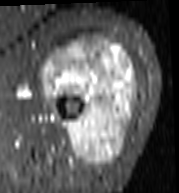
MRI of an extremity soft-tissue mass, one axial slice; position 69 of 103 along the scan axis; STIR; MR volume resampled by the dataset authors to the PET/CT grid (not the native acquisition matrix); 3.27 mm slice thickness; 179 × 193 image matrix, field of view 175 × 188 mm. Female patient. From the clinical record (not read from this slice): histological type: undifferentiated – high grade; grade: high; site of the primary tumour: left thigh.
Annotated regions visible in this slice (expert contour drawn on MRI and transferred to this co-registered scan by the dataset authors):
- gross tumour volume including surrounding oedema: bounding box (x1, y1, x2, y2) in pixels: (43, 35, 140, 168)
- gross tumour volume (mass): (43, 35, 138, 168)